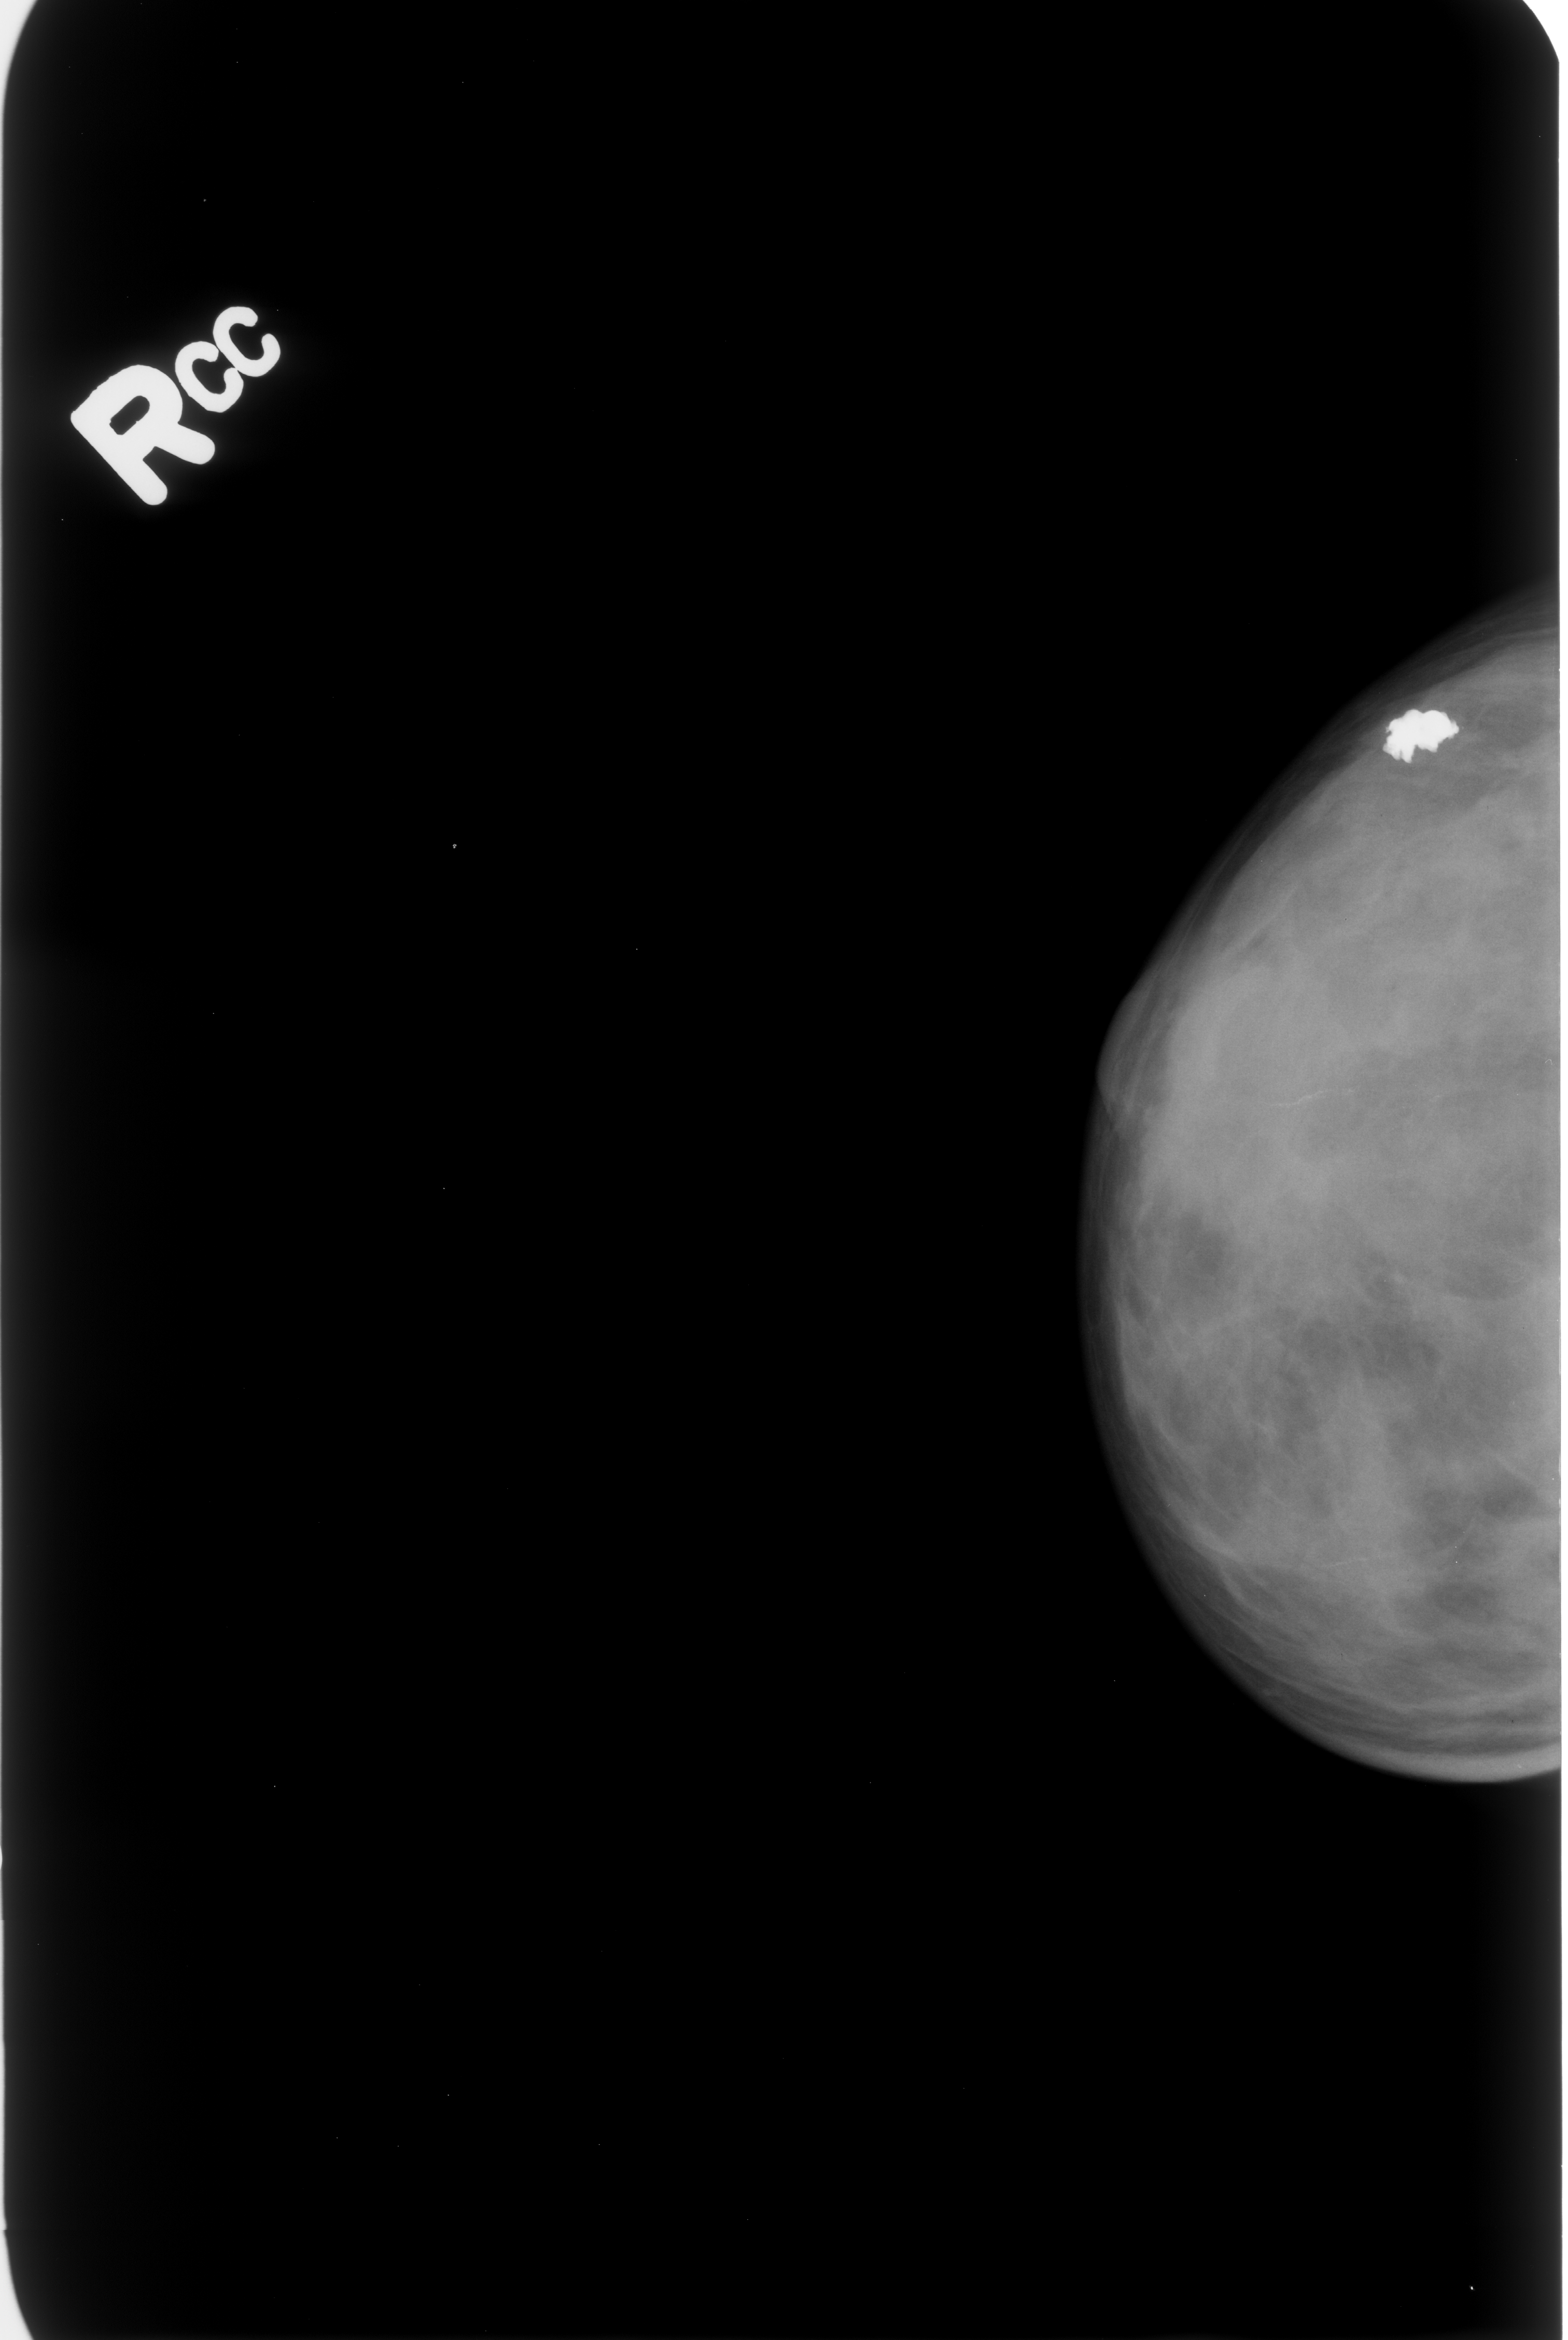
Scanned film-screen mammogram. Right breast. Craniocaudal (CC) view. 1568 × 2340 image matrix.
Expert-marked regions of interest on this film, with their recorded descriptors:
- calcifications, morphology coarse; BI-RADS assessment category 2; outcome (as recorded, no biopsy): benign without callback (not worked up further): box from (x=1368, y=692) to (x=1482, y=781) px